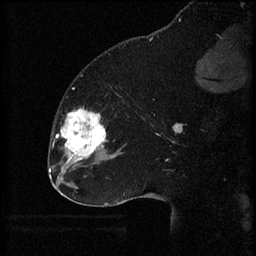
Breast MRI (dynamic contrast-enhanced), one sagittal slice. Slice 22 of 60 in the series (ordered by position). 3 images stored at this slice position (order not interpretable as contrast timing). 1.5 T. TE 4.2 ms, TR 8.2 ms. 256 × 256 image matrix. Female patient, age 32 years.
Outlined on this slice (semi-automatically segmented with operator editing):
- analysis volume of interest (the breast-tissue region the enhancement analysis was run in; not a lesion): bounding box [x1, y1, x2, y2] px = [58, 108, 111, 165]
- tumour enhancement mask (voxels above the 70 % enhancement threshold inside the analysis volume of interest): [61, 108, 106, 165]